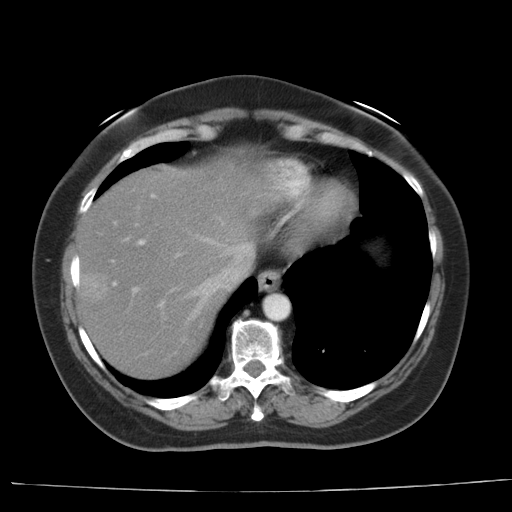
Contrast-enhanced abdominal CT, one axial slice; position 31 of 44 along the scan axis; 140 kVp; intravenous contrast given; soft-tissue window (W 400 / L 40 HU); 5 mm slice thickness; 512 × 512 image matrix, field of view 373 × 373 mm. Female patient. Case-level facts recorded for this patient, not image findings: diagnosis: colorectal cancer liver metastases, imaged before liver resection.
Outlined on this slice (outlined manually by an expert reader):
- hepatic veins: bounding box <158,238,253,323> (left, top, right, bottom; pixels)
- liver: <79,148,277,380>
- planned liver remnant (the part of the liver to remain after resection): <108,149,279,276>
- portal vein (with intrahepatic branches): <111,195,153,294>